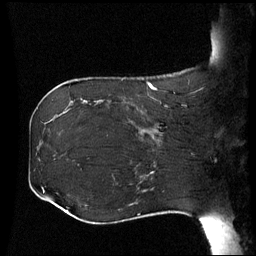
Breast MRI (dynamic contrast-enhanced), one sagittal slice; position 19 of 60 along the scan axis; dynamic contrast-enhanced series, image 2 of 3 at this slice position (ordered by acquisition); 1.5 T; TE 4.2 ms, TR 8.9 ms; 256 × 256 image matrix, field of view 230 × 230 mm. Female patient, age 42 years. Case-level facts recorded for this patient, not image findings: setting: breast cancer imaged before/during neoadjuvant chemotherapy; receptor status: HER2-positive.
Outlined on this slice (semi-automatically segmented with operator editing):
- analysis volume of interest (the breast-tissue region the enhancement analysis was run in; not a lesion): bounding box (x1, y1, x2, y2) in pixels: (106, 102, 173, 150)
- tumour enhancement mask (voxels above the 70 % enhancement threshold inside the analysis volume of interest): (139, 132, 153, 137)